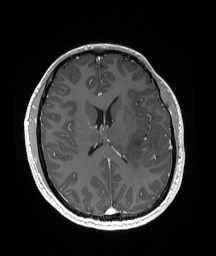
Brain MRI from a brain-tumour surgery series, one axial slice; slice 77 of 192 in the series (ordered by position); T1-weighted post-contrast; 1 mm slice thickness; 216 × 256 image matrix, field of view 211 × 250 mm. From the clinical record (not read from this slice): histopathology: Glioneuronal tumor; WHO grade: 2.
Annotated regions visible in this slice (outlined manually by an expert reader):
- tumour: bounding box <143,144,151,154> (left, top, right, bottom; pixels)